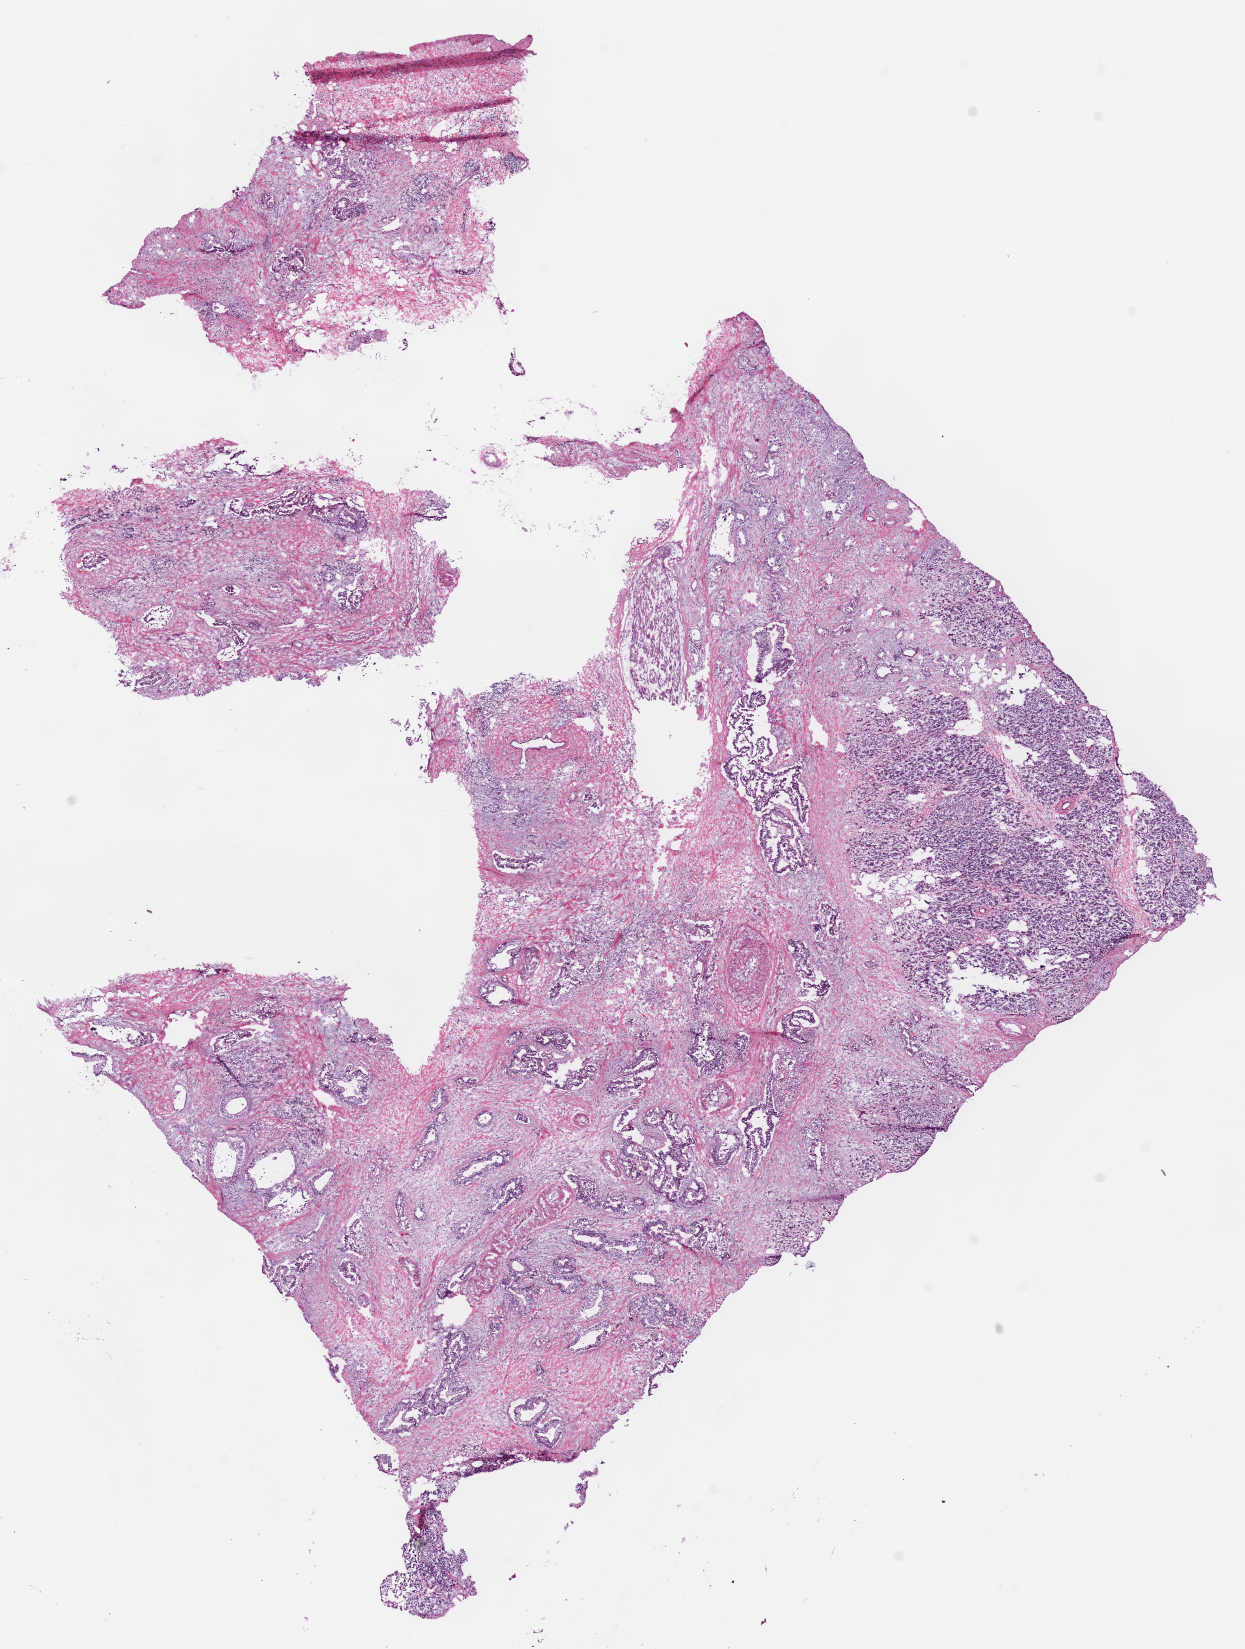
Hematoxylin and eosin (H&E) stained whole-slide image, low-resolution overview of the scanned area, about 9.8 x 13.0 mm (acquisition: 40x scan); frozen section from the bottom of the tissue portion; primary tumour sample from the pancreas. Male patient; age at initial diagnosis 80 years. Slide review estimates, as recorded: tumour cells 74%, tumour nuclei 61%.
Histologic diagnosis: Infiltrating duct carcinoma, NOS (head of pancreas).